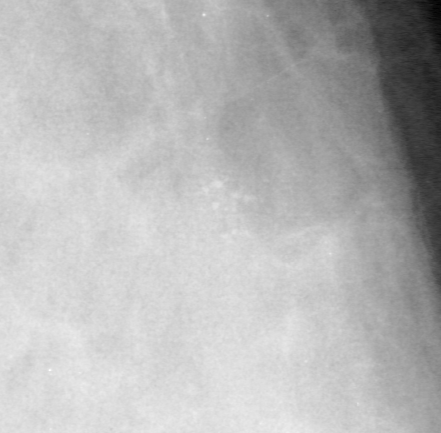
Region of interest cut from a scanned film mammogram (one marked finding), right breast, MLO view, BI-RADS breast density category 4 (scale 1–4).
- Finding: calcifications, morphology pleomorphic, distribution clustered; BI-RADS assessment category 4; pathology (as recorded): benign.